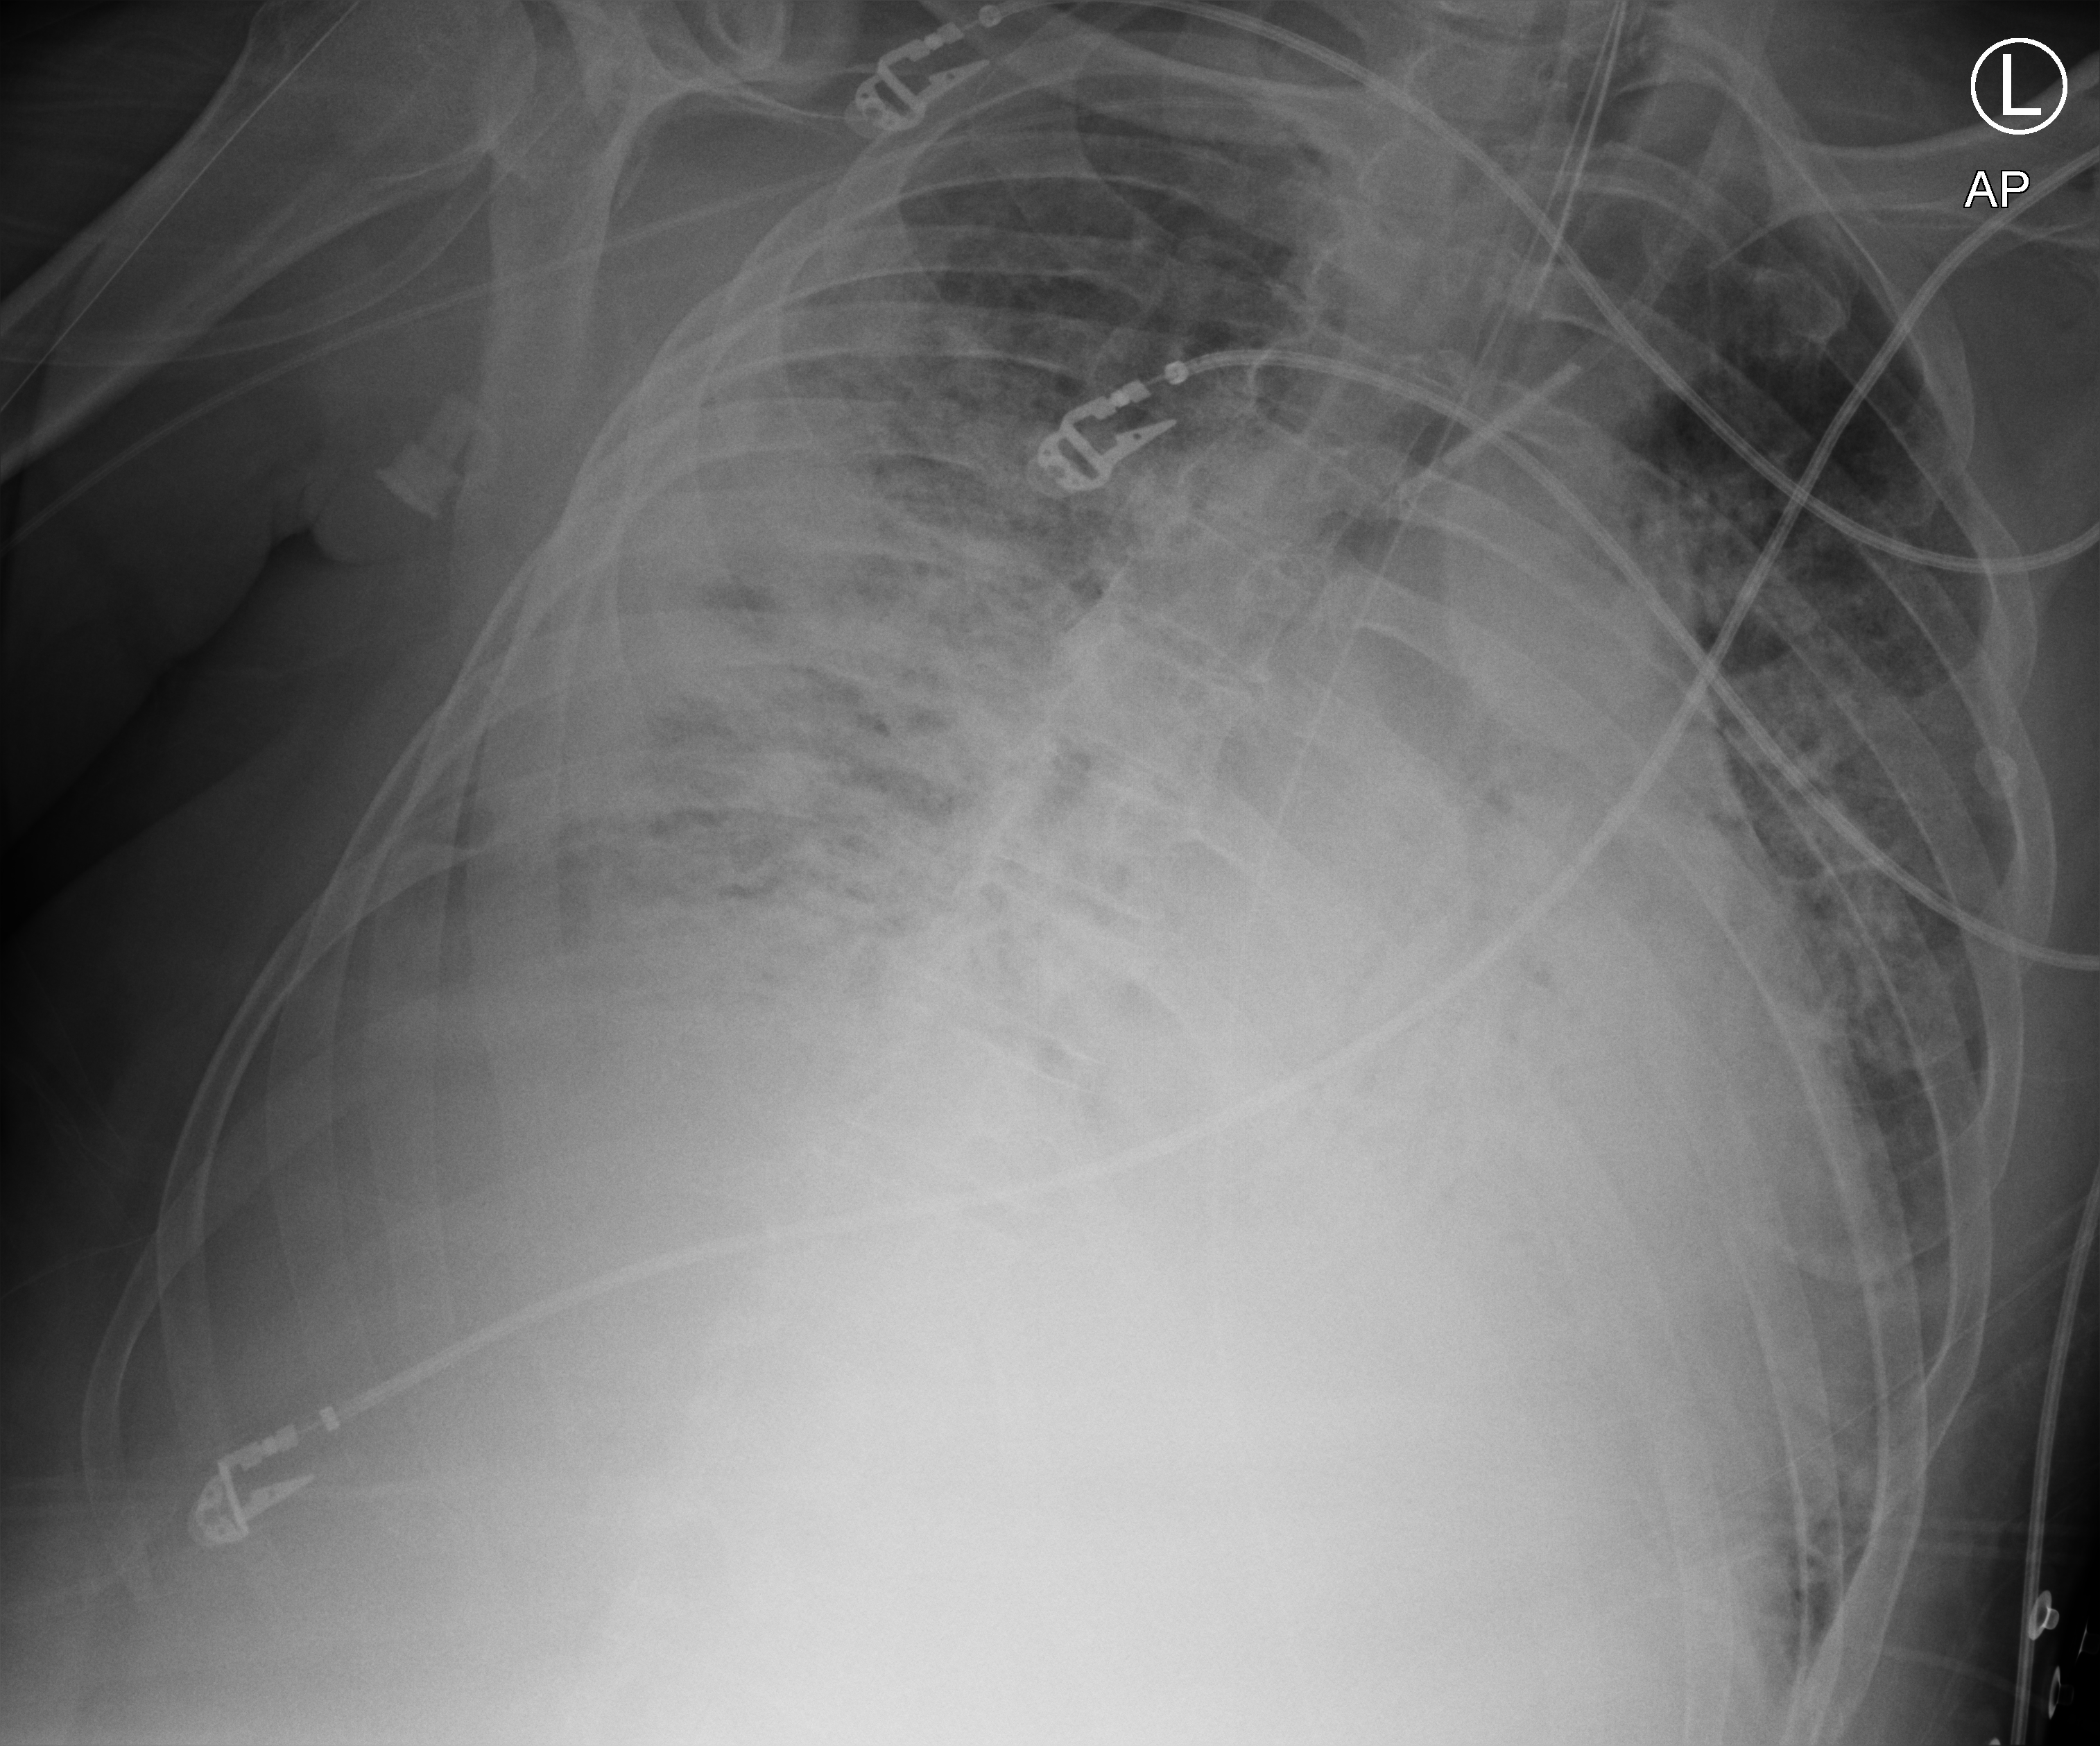
Bedside chest radiograph (computed radiography); anteroposterior (AP) projection. Male patient hospitalised with COVID-19, age 18–59 years.
Admission-level facts for this patient (not findings on this image; timing relative to this image not recorded): mechanically ventilated during this hospital stay: yes; smoking status (admission record): never; admitted to intensive care during this hospital stay: yes.